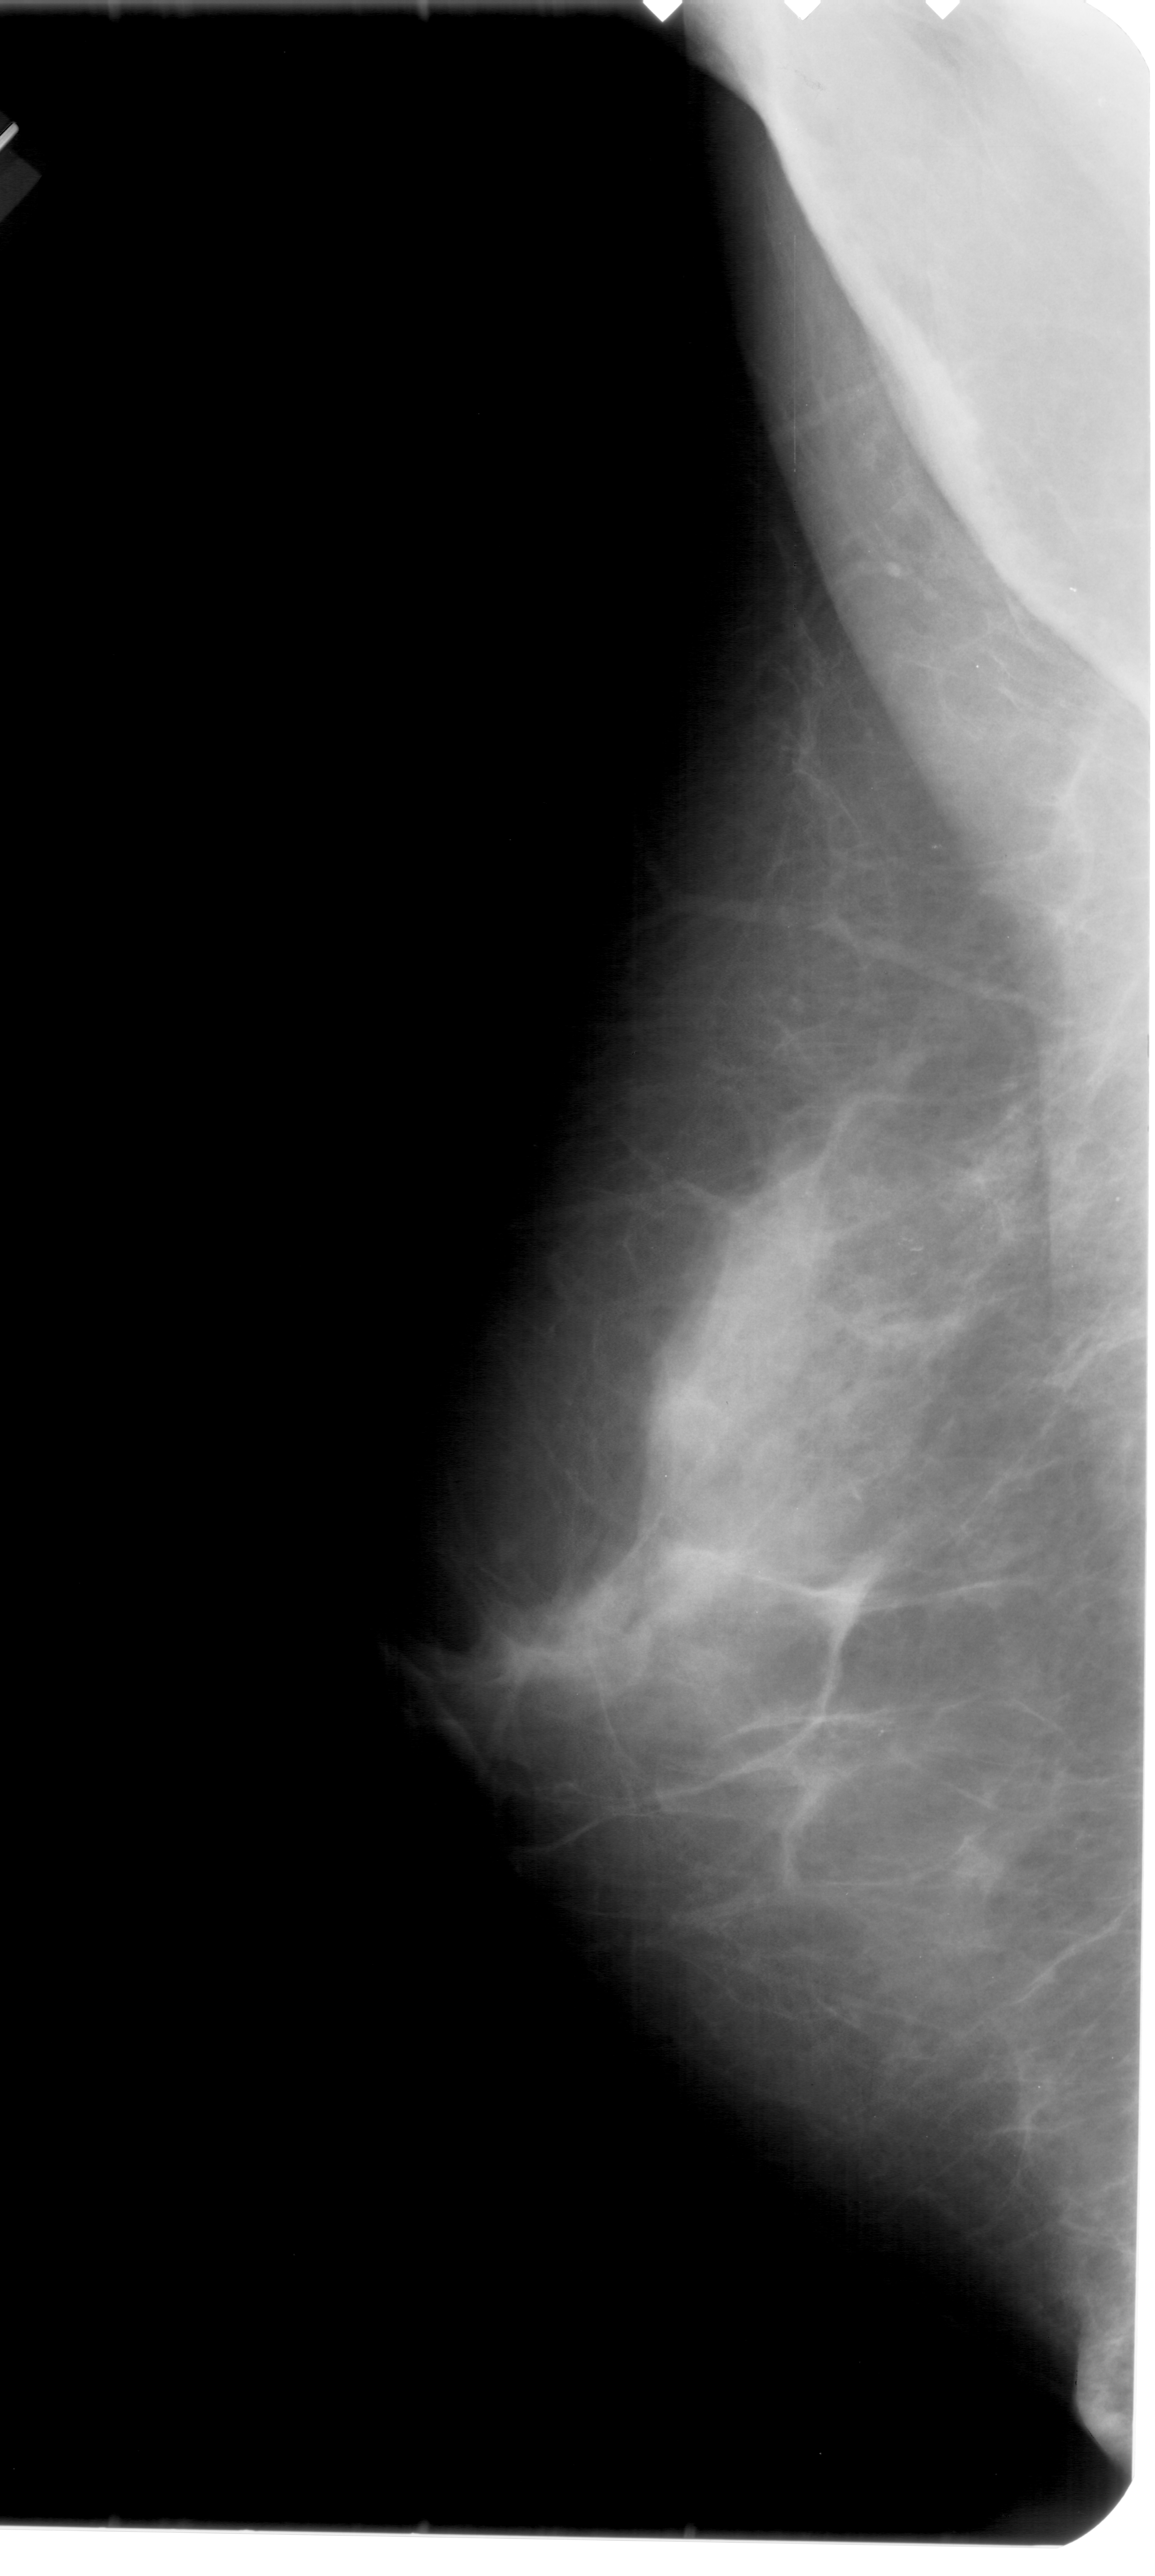
Mammogram (digitized film). Left breast. Mediolateral oblique (MLO) view. BI-RADS breast density category 4 (scale 1–4). 1155 × 2576 image matrix.
Expert-marked regions of interest on this image (one box per marked abnormality):
- calcifications, morphology pleomorphic, distribution clustered; BI-RADS assessment category 4; subtlety rating 3 on a 1 (subtle) to 5 (obvious) scale; pathology (as recorded): benign: box from (x=894, y=1217) to (x=945, y=1283) px